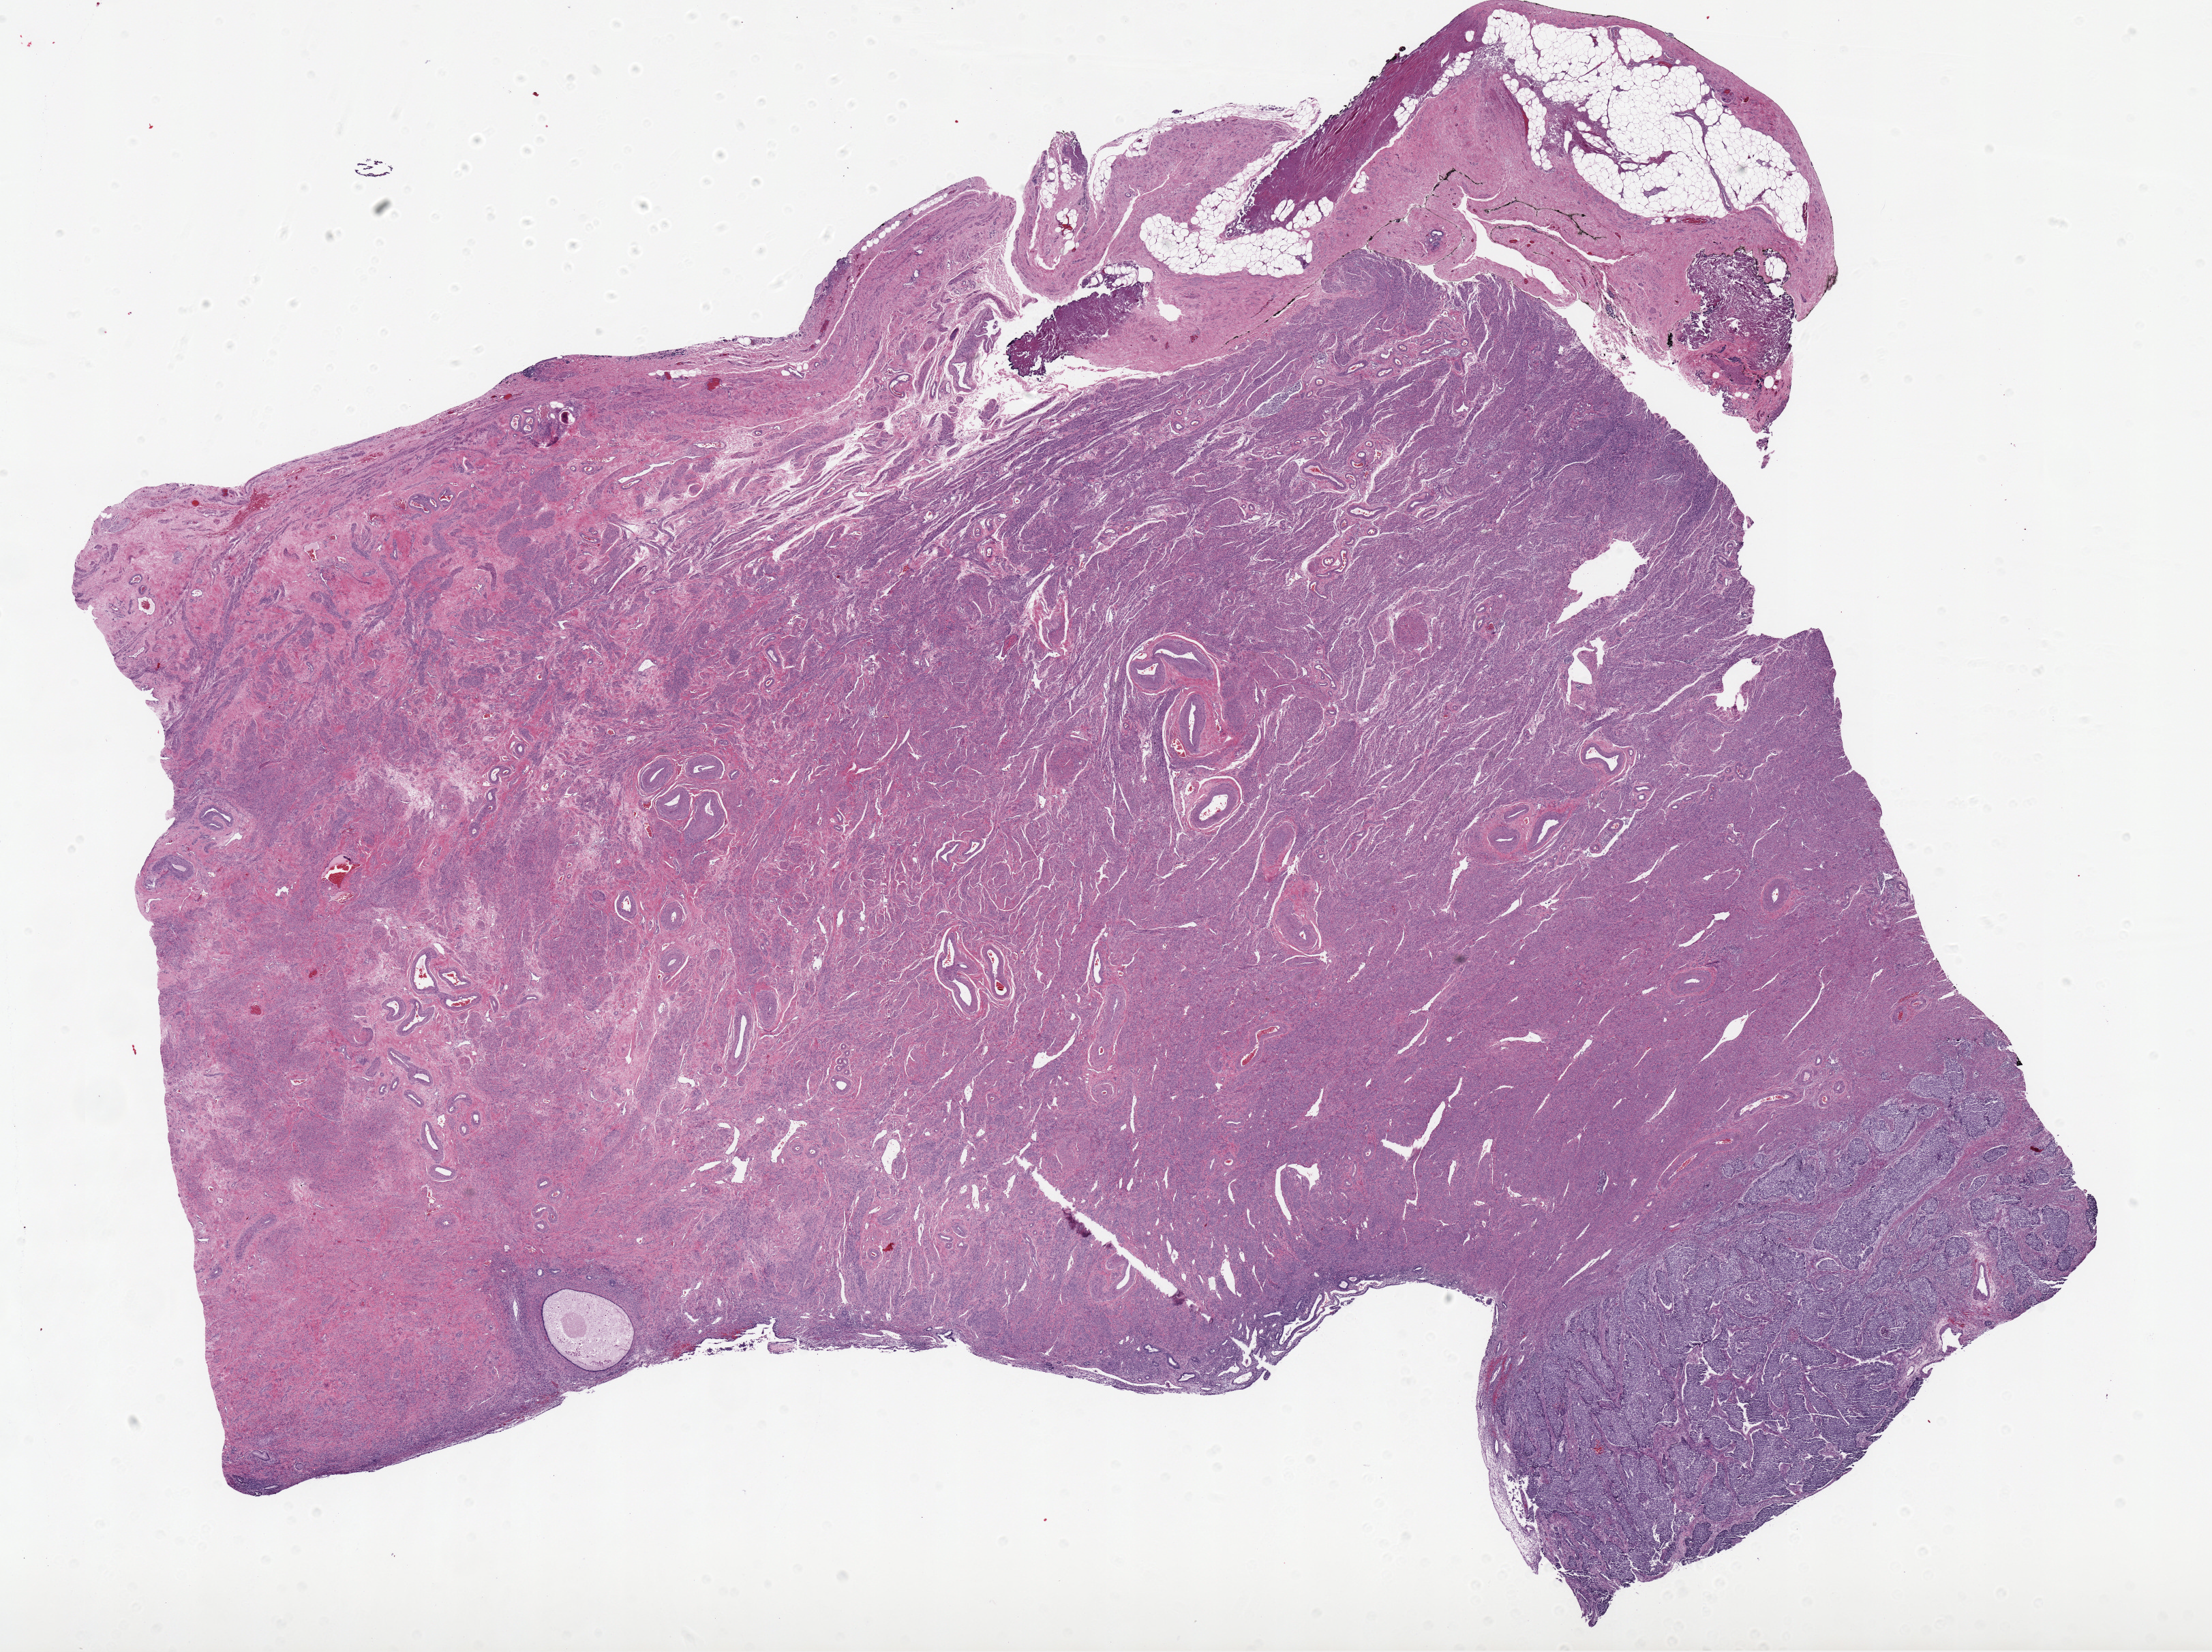
H&E whole-slide image — low-resolution overview of the scanned area, about 25.9 x 19.3 mm; FFPE section; sample: primary tumour, uterus. Female patient; age at initial diagnosis 63 years. Histologic grade: G3 (poorly differentiated).
Lymph nodes positive (case pathology): 0 of 20 examined. FIGO stage: IB. Histologic diagnosis: Endometrioid adenocarcinoma, NOS (endometrium).